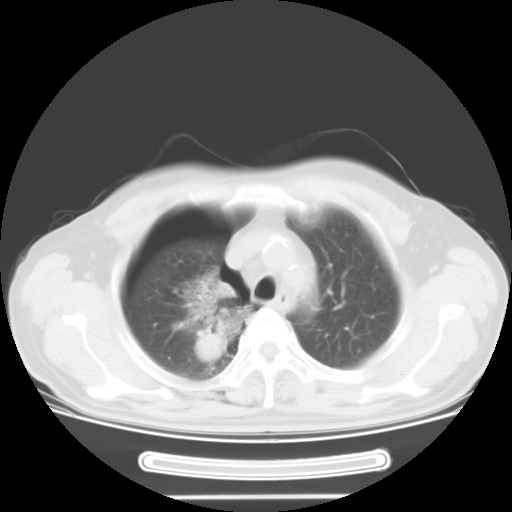
Chest CT, one axial slice; position 23 of 29 along the scan axis; 120 kVp; lung window (W 1500 / L -600 HU); 512 × 512 image matrix, field of view 376 × 376 mm. Male patient, age 61 years. Case-level facts recorded for this patient, not image findings: clinical TNM (as recorded): T1c N3 M1b.
Structures marked on this image (rectangle marked by the reading radiologist):
- lung tumour (recorded histology: adenocarcinoma): bounding box (x1, y1, x2, y2) in pixels: (167, 264, 255, 368)